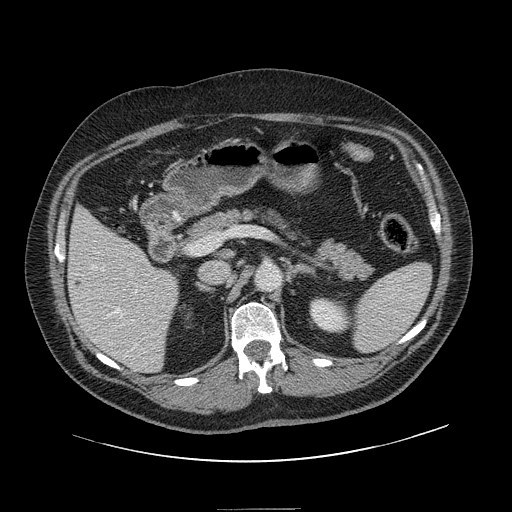
Contrast-enhanced abdominal CT, one axial slice; position 73 of 154 along the scan axis; intravenous contrast given; soft-tissue window (W 400 / L 40 HU); 2.5 mm slice thickness; 512 × 512 image matrix. Male patient, age 61 years. From the clinical record (not read from this slice): diagnosis: colorectal cancer liver metastases, imaged before liver resection; multiple liver metastases: yes; largest metastasis: 2.6 cm; disease in both lobes: yes.
Annotated regions visible in this slice (outlined manually by an expert reader):
- hepatic veins: box from (x=91, y=265) to (x=138, y=349) px
- liver: (x=69, y=210)–(x=178, y=372)
- planned liver remnant (the part of the liver to remain after resection): (x=70, y=210)–(x=178, y=366)
- portal vein (with intrahepatic branches): (x=131, y=319)–(x=134, y=321)
- liver metastasis: (x=77, y=281)–(x=83, y=288)